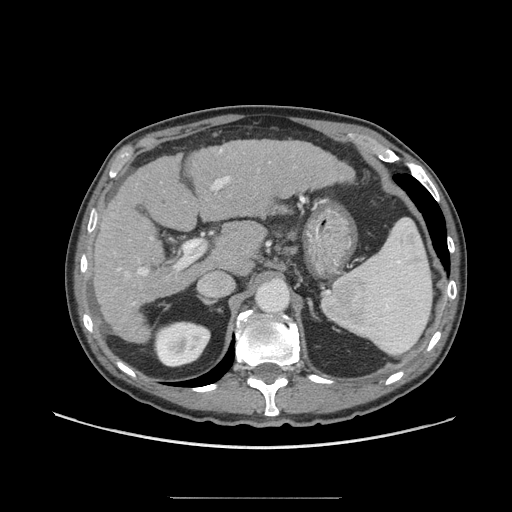
Contrast-enhanced abdominal CT (liver protocol), one axial slice; position 41 of 71 along the scan axis; reconstruction kernel STANDARD; soft-tissue window (W 400 / L 40 HU); 2.5 mm slice thickness; 512 × 512 image matrix, field of view 400 × 400 mm. From the clinical record (not read from this slice): diagnosis: hepatocellular carcinoma (patient treated with transarterial chemoembolisation; whether this scan precedes or follows treatment is not stated here); TNM stage (as recorded): Stage-I; Child-Pugh class: A; tumour size: 3.5 cm.
Outlined on this slice (semi-automatic segmentation, software-assisted and operator-edited):
- liver parenchyma outside the tumour (the mass and vessels are separate outlines, so this box may not span the whole liver): bounding box (x1, y1, x2, y2) in pixels: (92, 140, 354, 342)
- liver vessels: (117, 148, 230, 305)